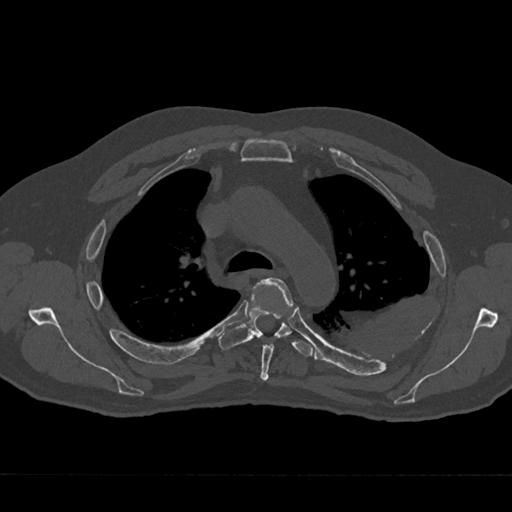
CT including the spine, one axial slice. Position 495 of 797 along the scan axis. Reconstruction kernel Br40s/3. Bone window (W 1800 / L 400 HU). 512 × 512 image matrix, field of view 377 × 377 mm. Male patient, age 75 years. Case-level facts recorded for this patient, not image findings: primary cancer: renal; vertebrae with lytic lesions (as recorded): T4.
Outlined on this slice (semi-automatic segmentation, software-assisted and operator-edited):
- T4 vertebra: bounding box <258,278,294,381> (left, top, right, bottom; pixels)
- T5 vertebra: <218,295,314,356>